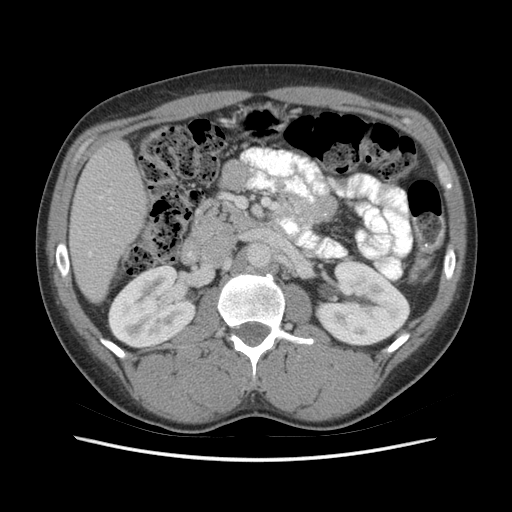
Contrast-enhanced abdominal CT (liver protocol), one axial slice; position 20 of 73 along the scan axis; 140 kVp; soft-tissue window (W 400 / L 40 HU); 2.5 mm slice thickness; 512 × 512 image matrix, field of view 360 × 360 mm. Case-level facts recorded for this patient, not image findings: diagnosis: hepatocellular carcinoma (patient treated with transarterial chemoembolisation; whether this scan precedes or follows treatment is not stated here); TNM stage (as recorded): Stage-IIIA.
Structures marked on this image (semi-automatic segmentation, software-assisted and operator-edited):
- liver parenchyma outside the tumour (the mass and vessels are separate outlines, so this box may not span the whole liver): bounding box (x1, y1, x2, y2) in pixels: (70, 140, 146, 302)
- liver vessels: (90, 197, 111, 254)